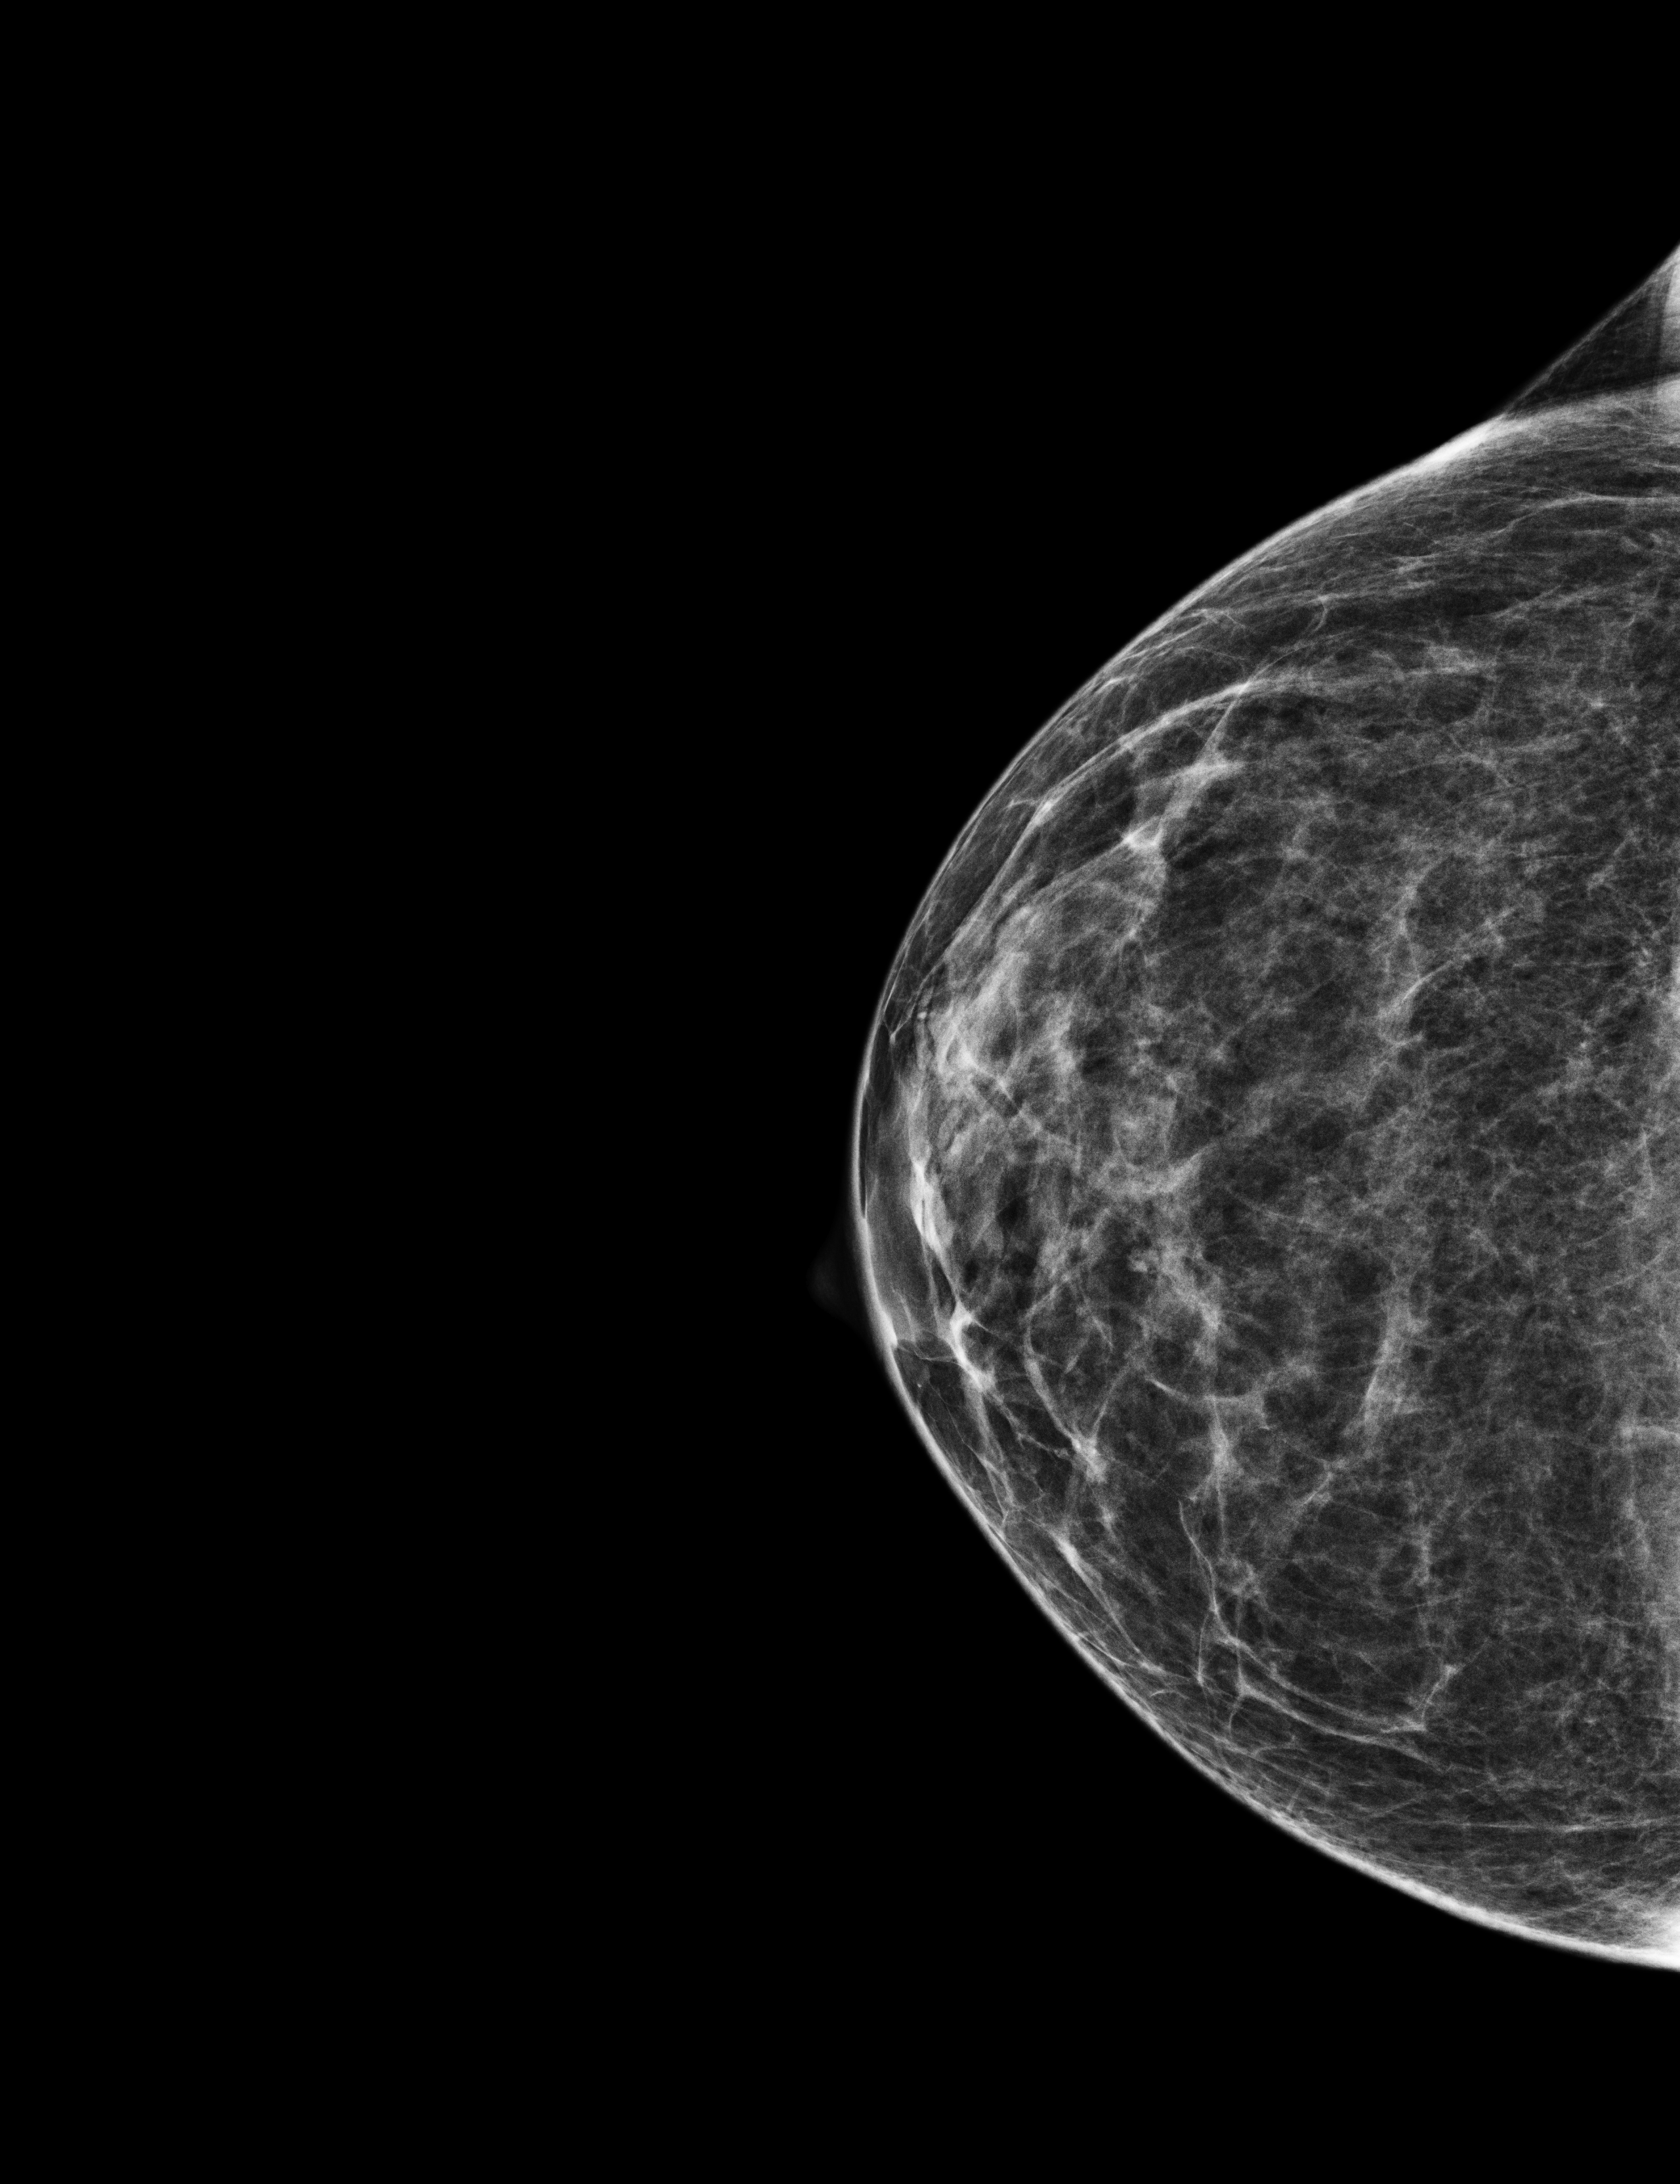
Screening examination; compressed breast thickness 36 mm; system: Selenia Dimensions. Patient aged 69 years (female).
Image type: full-field digital mammogram. Breast: right. Projection: cranio-caudal projection.